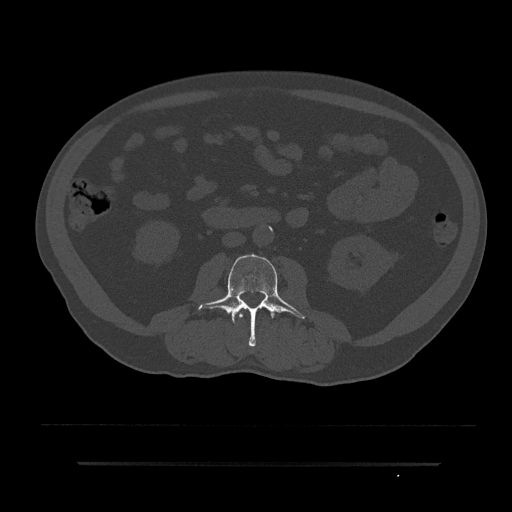
CT including the spine, one axial slice. Position 11 of 797 along the scan axis. 120 kVp. Bone window (W 1800 / L 400 HU). 0.5 mm slice thickness. 512 × 512 image matrix, field of view 464 × 464 mm. Patient: male, 59 years. Case-level facts recorded for this patient, not image findings: primary cancer: bile ducts.
Structures marked on this image (semi-automatic segmentation, software-assisted and operator-edited):
- L2 vertebra: bounding box <239,308,244,319> (left, top, right, bottom; pixels)
- L3 vertebra: <198,254,306,346>